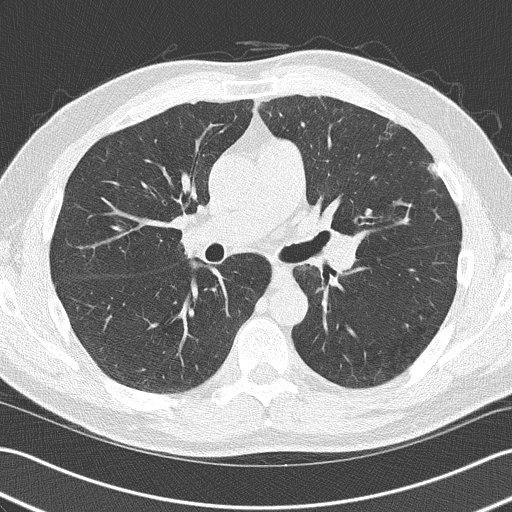
Axial slice from a low-dose chest CT screening exam; baseline annual screen; lung window (W 1500 / L -600 HU); lung (sharp) reconstruction kernel (B50f); 512 × 512 image matrix. Male, age 58 years at enrolment. Current smoker at enrolment.
Expert reader's lesion annotation, bounding box (x1, y1, x2, y2) in pixels: (416, 154, 458, 189). Reader record for this screening exam (exam-level; its link to the box is not recorded): non-calcified nodule or mass ≥4 mm, lingula, 10 × 6 mm, mixed attenuation. Participant outcome: lung cancer diagnosed 258 days after this screen — squamous cell carcinoma, NOS, lingula, poorly differentiated (G3), stage IIIB (AJCC 6th edition).